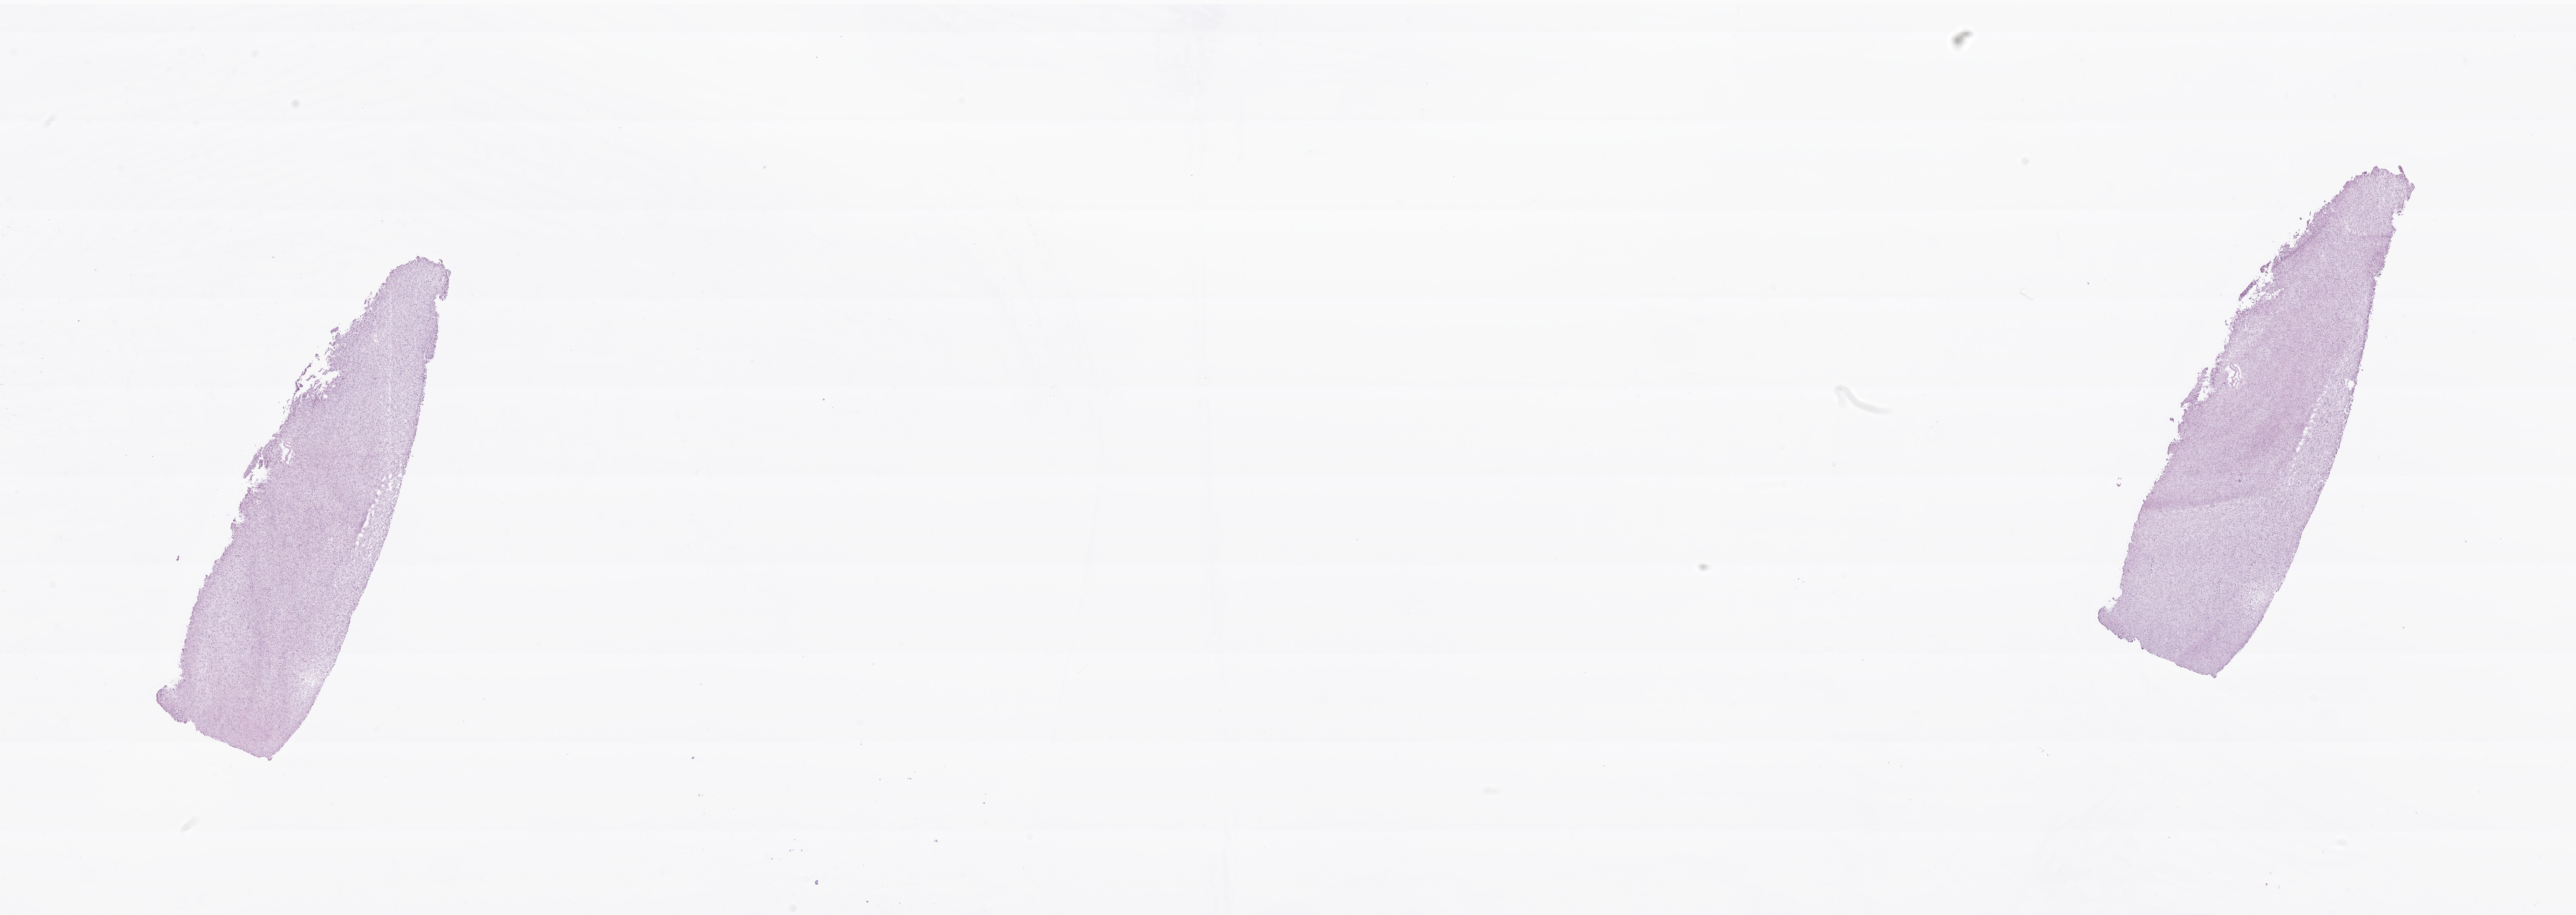
Digitized H&E-stained section of tumor tissue from the brain — low-resolution overview of the scanned area, about 30.9 x 11.0 mm; frozen section. Patient male; age 110 months (9 years 2 months).
- diagnosis: Glioma, malignant